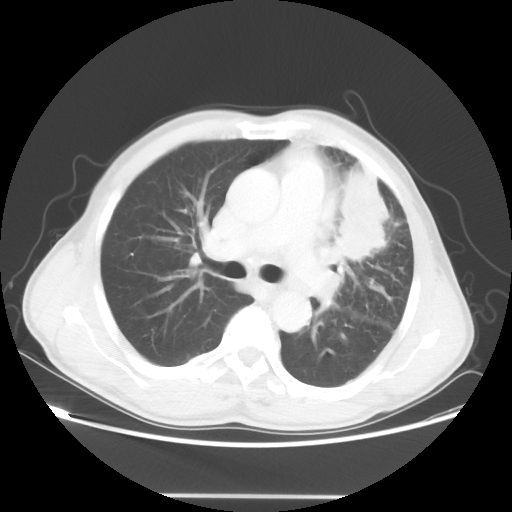
Chest CT, one axial slice; position 32 of 55 along the scan axis; reconstruction kernel STANDARD; lung window (W 1500 / L -600 HU); 5 mm slice thickness; 512 × 512 image matrix, field of view 398 × 398 mm. Patient: male, 60 years. Case-level facts recorded for this patient, not image findings: clinical TNM (as recorded): T3 N3 M0.
Structures marked on this image (bounding box drawn by a radiologist):
- lung tumour (recorded histology: adenocarcinoma): bounding box (x1, y1, x2, y2) in pixels: (338, 163, 389, 267)